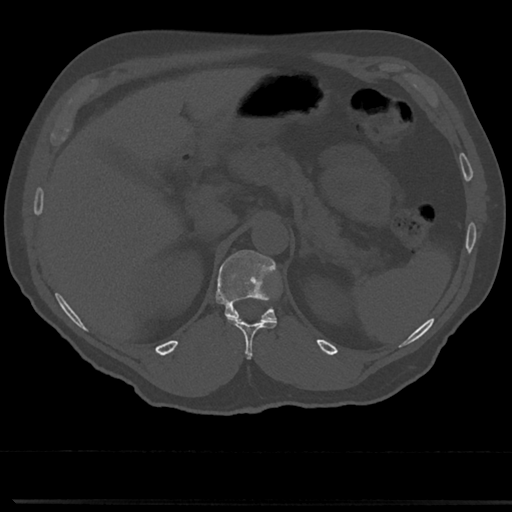
CT including the spine, one axial slice; position 173 of 817 along the scan axis; 120 kVp; bone window (W 1800 / L 400 HU); 0.5 mm slice thickness; 512 × 512 image matrix, field of view 355 × 355 mm. Male patient, age 61 years. Case-level facts recorded for this patient, not image findings: primary cancer: prostate.
Annotated regions visible in this slice (semi-automatically segmented with operator editing):
- T11 vertebra: bounding box <229,318,275,358> (left, top, right, bottom; pixels)
- T12 vertebra: <215,250,285,323>